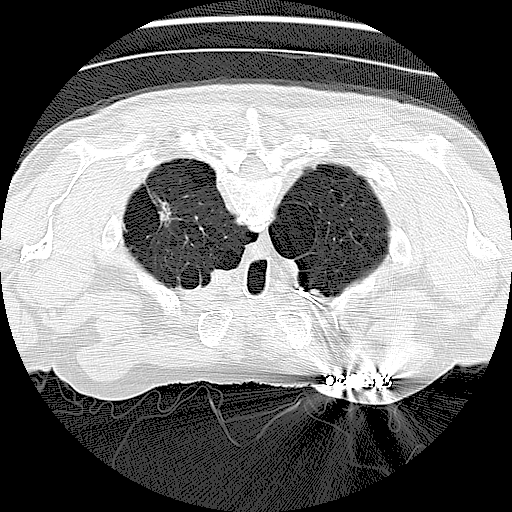
Low-dose screening chest CT, axial slice. First (baseline) screen. Lung window (W 1500 / L -600 HU). Slice 22 of 138 in the series. 512 × 512 image matrix. Male, age 73 years at enrolment.
• Expert reader's lesion annotation, bounding box (x1, y1, x2, y2) in pixels: (138, 193, 185, 238).
• The screening reader recorded 2 non-calcified nodules or masses ≥4 mm on this exam; which of them this box marks is not recorded.
• Official screen result: positive, change unspecified: nodule(s) >= 4 mm or enlarging nodule(s), mass(es), or other non-specific abnormalities suspicious for lung cancer.
• Later outcome: lung cancer diagnosed 308 days after this screen — neoplasm, malignant, stage IV (AJCC 6th edition).